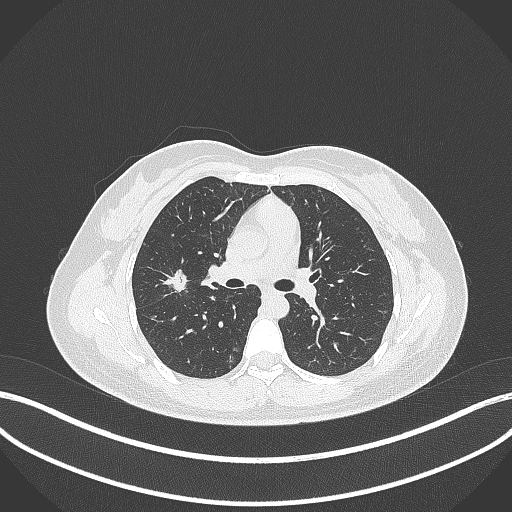
Chest CT, one axial slice. Position 199 of 307 along the scan axis. Reconstruction kernel B70f. Lung window (W 1500 / L -600 HU). 1 mm slice thickness. 512 × 512 image matrix, field of view 400 × 400 mm. Female patient, age 33 years. Case-level facts recorded for this patient, not image findings: clinical TNM (as recorded): T1c N0 M0; histopathological grade: G2-G3.
Structures marked on this image (bounding box drawn by a radiologist):
- lung tumour (recorded histology: adenocarcinoma): bounding box <164,264,189,299> (left, top, right, bottom; pixels)